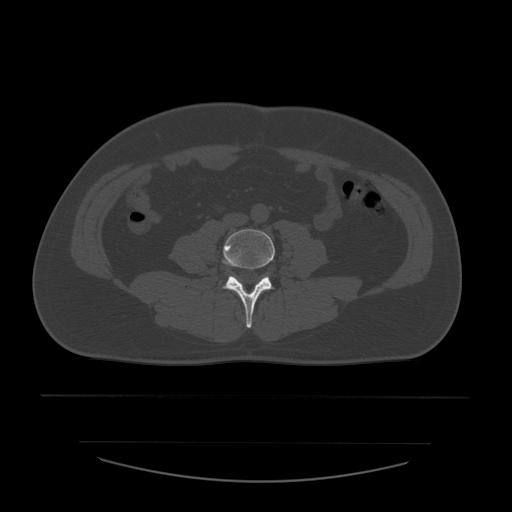
CT including the spine, one axial slice. Slice 142 of 532 in the series (ordered by position). Reconstruction kernel STANDARD. Bone window (W 1800 / L 400 HU). 1.25 mm slice thickness. 512 × 512 image matrix, field of view 441 × 441 mm. Patient age 44 years. From the clinical record (not read from this slice): primary cancer: soft tissue sarcoma.
Annotated regions visible in this slice (semi-automatically segmented with operator editing):
- L4 vertebra: bounding box [x1, y1, x2, y2] px = [224, 229, 275, 328]